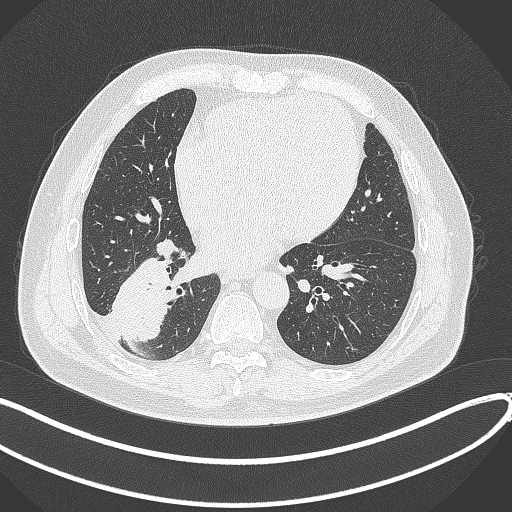
Chest CT, one axial slice. Slice 137 of 360 in the series (ordered by position). Reconstruction kernel B70f. 120 kVp. Lung window (W 1500 / L -600 HU). 1 mm slice thickness. 512 × 512 image matrix, field of view 400 × 400 mm. Male patient, age 59 years.
Structures marked on this image (rectangle marked by the reading radiologist):
- lung tumour (recorded histology: adenocarcinoma): bounding box <108,255,182,346> (left, top, right, bottom; pixels)